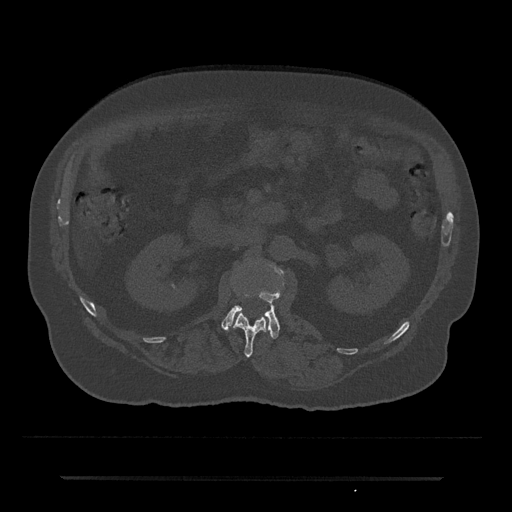
CT including the spine, one axial slice; slice 39 of 797 in the series (ordered by position); reconstruction kernel Br40s/3; 120 kVp; bone window (W 1800 / L 400 HU); 0.5 mm slice thickness; 512 × 512 image matrix, field of view 437 × 437 mm. Patient: male, 69 years. From the clinical record (not read from this slice): primary cancer: prostate.
Structures marked on this image (semi-automatic segmentation, software-assisted and operator-edited):
- L1 vertebra: bounding box (x1, y1, x2, y2) in pixels: (233, 313, 268, 357)
- L2 vertebra: (222, 266, 284, 339)